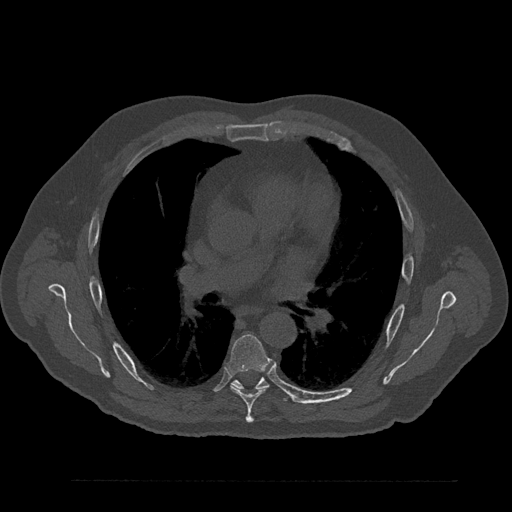
CT including the spine, one axial slice. Reconstruction kernel Br40s/3. 120 kVp. Bone window (W 1800 / L 400 HU). 0.5 mm slice thickness. 512 × 512 image matrix, field of view 430 × 430 mm. Patient: male, 61 years. Case-level facts recorded for this patient, not image findings: primary cancer: prostate.
Annotated regions visible in this slice (semi-automatically segmented with operator editing):
- T6 vertebra: bounding box [x1, y1, x2, y2] px = [228, 334, 271, 423]
- T7 vertebra: [233, 377, 288, 402]